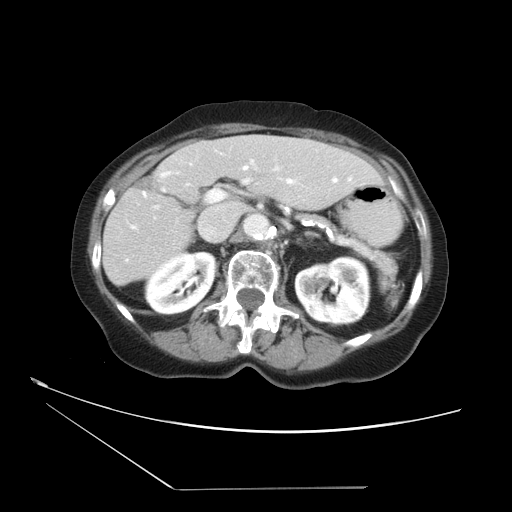
Contrast-enhanced abdominal CT, one axial slice. Position 18 of 36 along the scan axis. 120 kVp. Intravenous contrast given. Soft-tissue window (W 400 / L 40 HU). 5 mm slice thickness. 512 × 512 image matrix. Female patient, age 81 years. Case-level facts recorded for this patient, not image findings: diagnosis: colorectal cancer liver metastases, imaged before liver resection; multiple liver metastases: no; largest metastasis: 1.6 cm; disease in both lobes: no.
Annotated regions visible in this slice (expert manual segmentation):
- hepatic veins: bounding box (x1, y1, x2, y2) in pixels: (132, 161, 337, 229)
- liver: (103, 136, 384, 285)
- planned liver remnant (the part of the liver to remain after resection): (103, 138, 383, 284)
- portal vein (with intrahepatic branches): (143, 180, 248, 203)